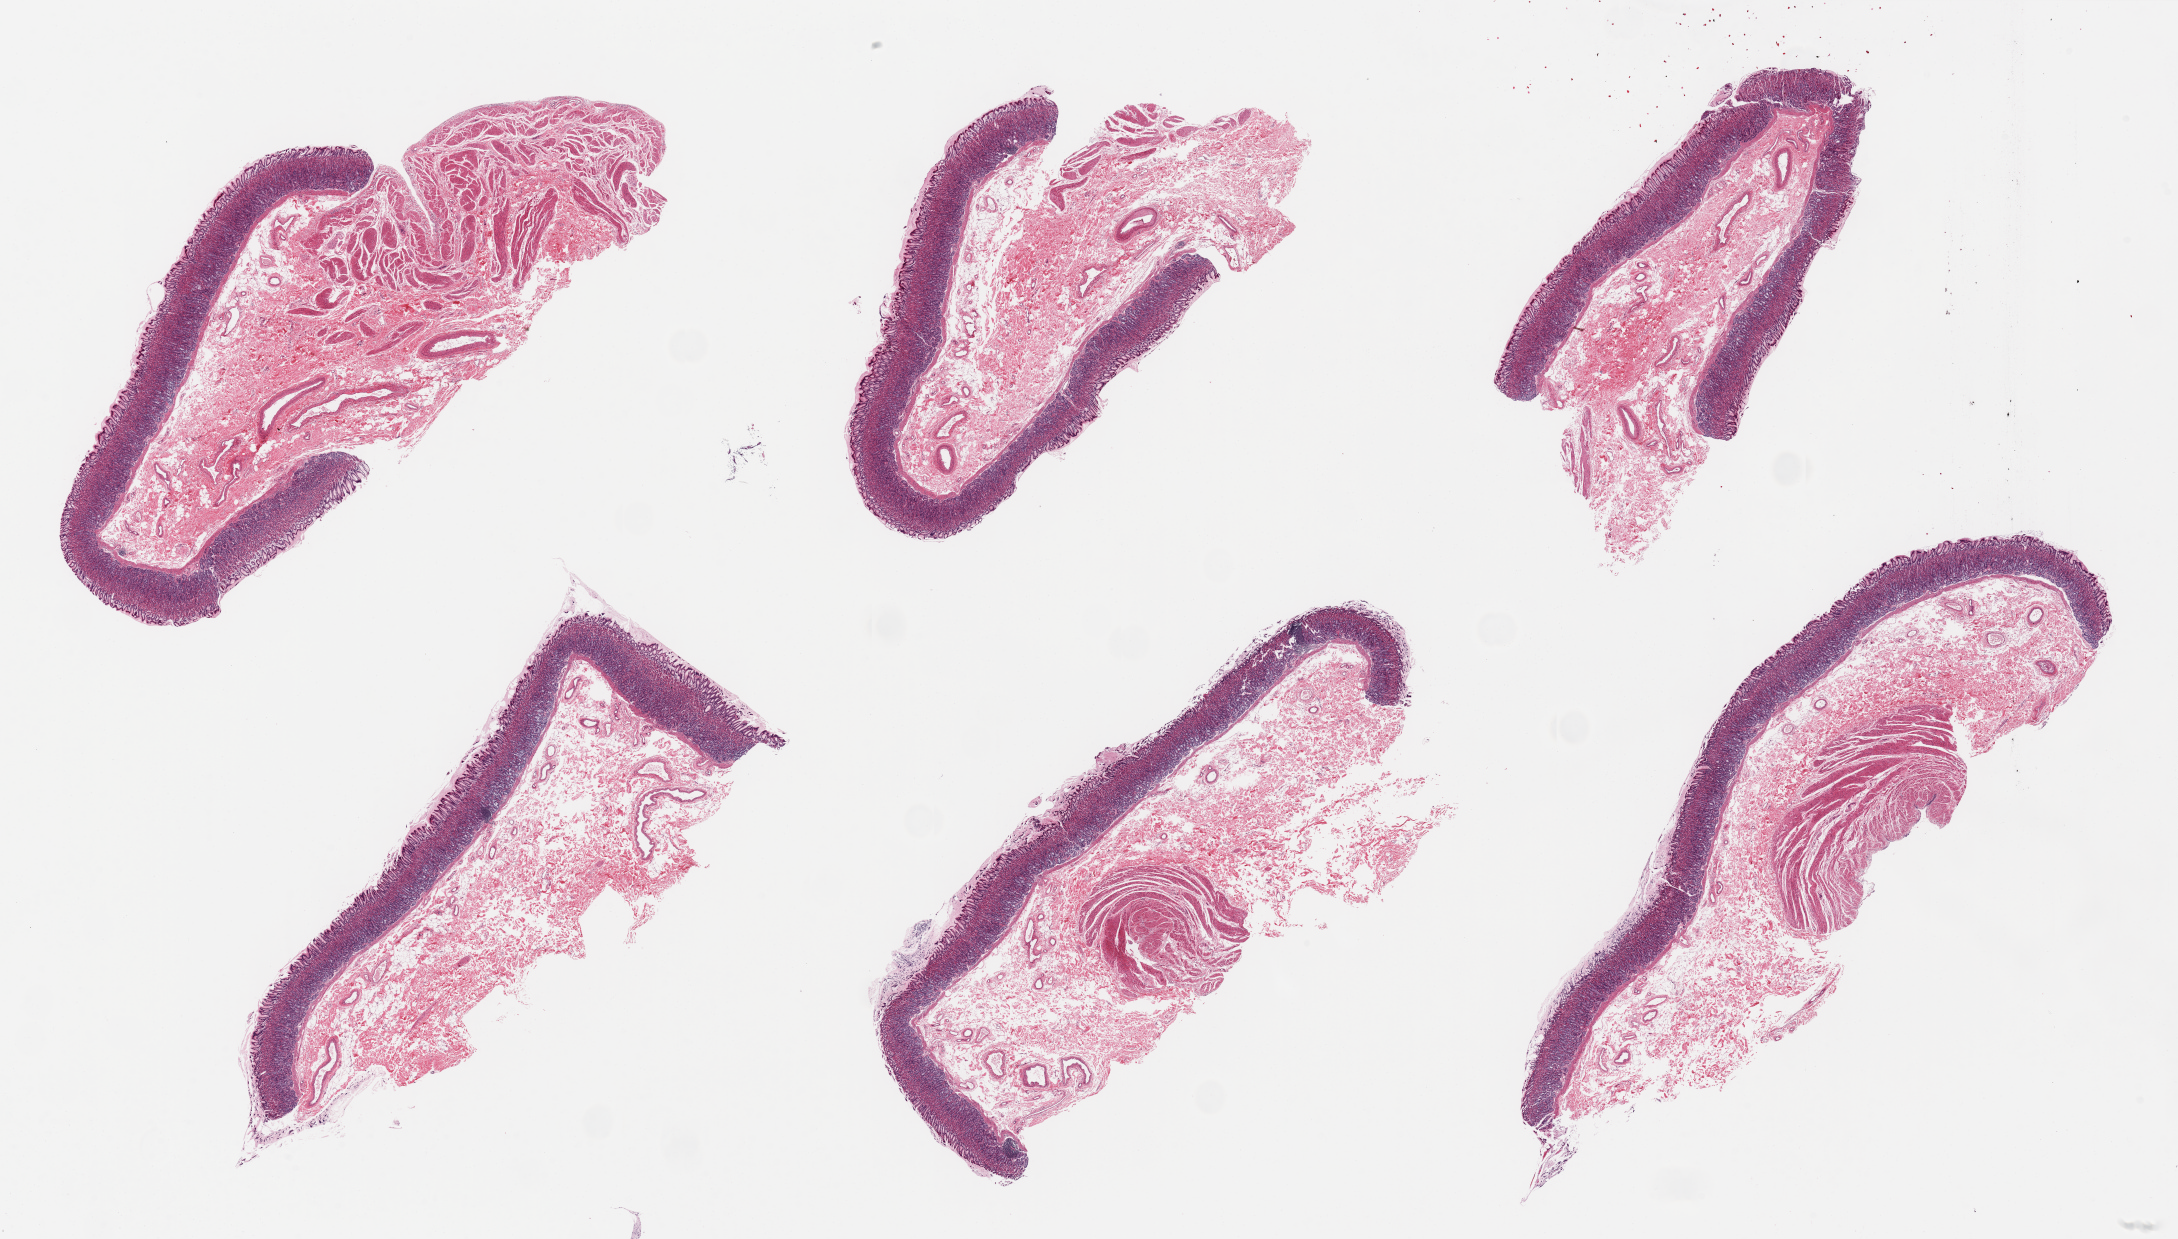
Whole-slide image, H&E stain, low-resolution overview of the scanned area, about 34.5 x 19.6 mm (from a 20x scan). PAXgene-fixed paraffin-embedded (PFPE) section. Sampled site (target tissue): stomach. Tissue donor sample. Donor: female.
Reviewer comment on this tissue sample: 6 pieces; mucosa well-preserved, ~0.6-0.8mm, ~15% of thickness. Excellent specimen.